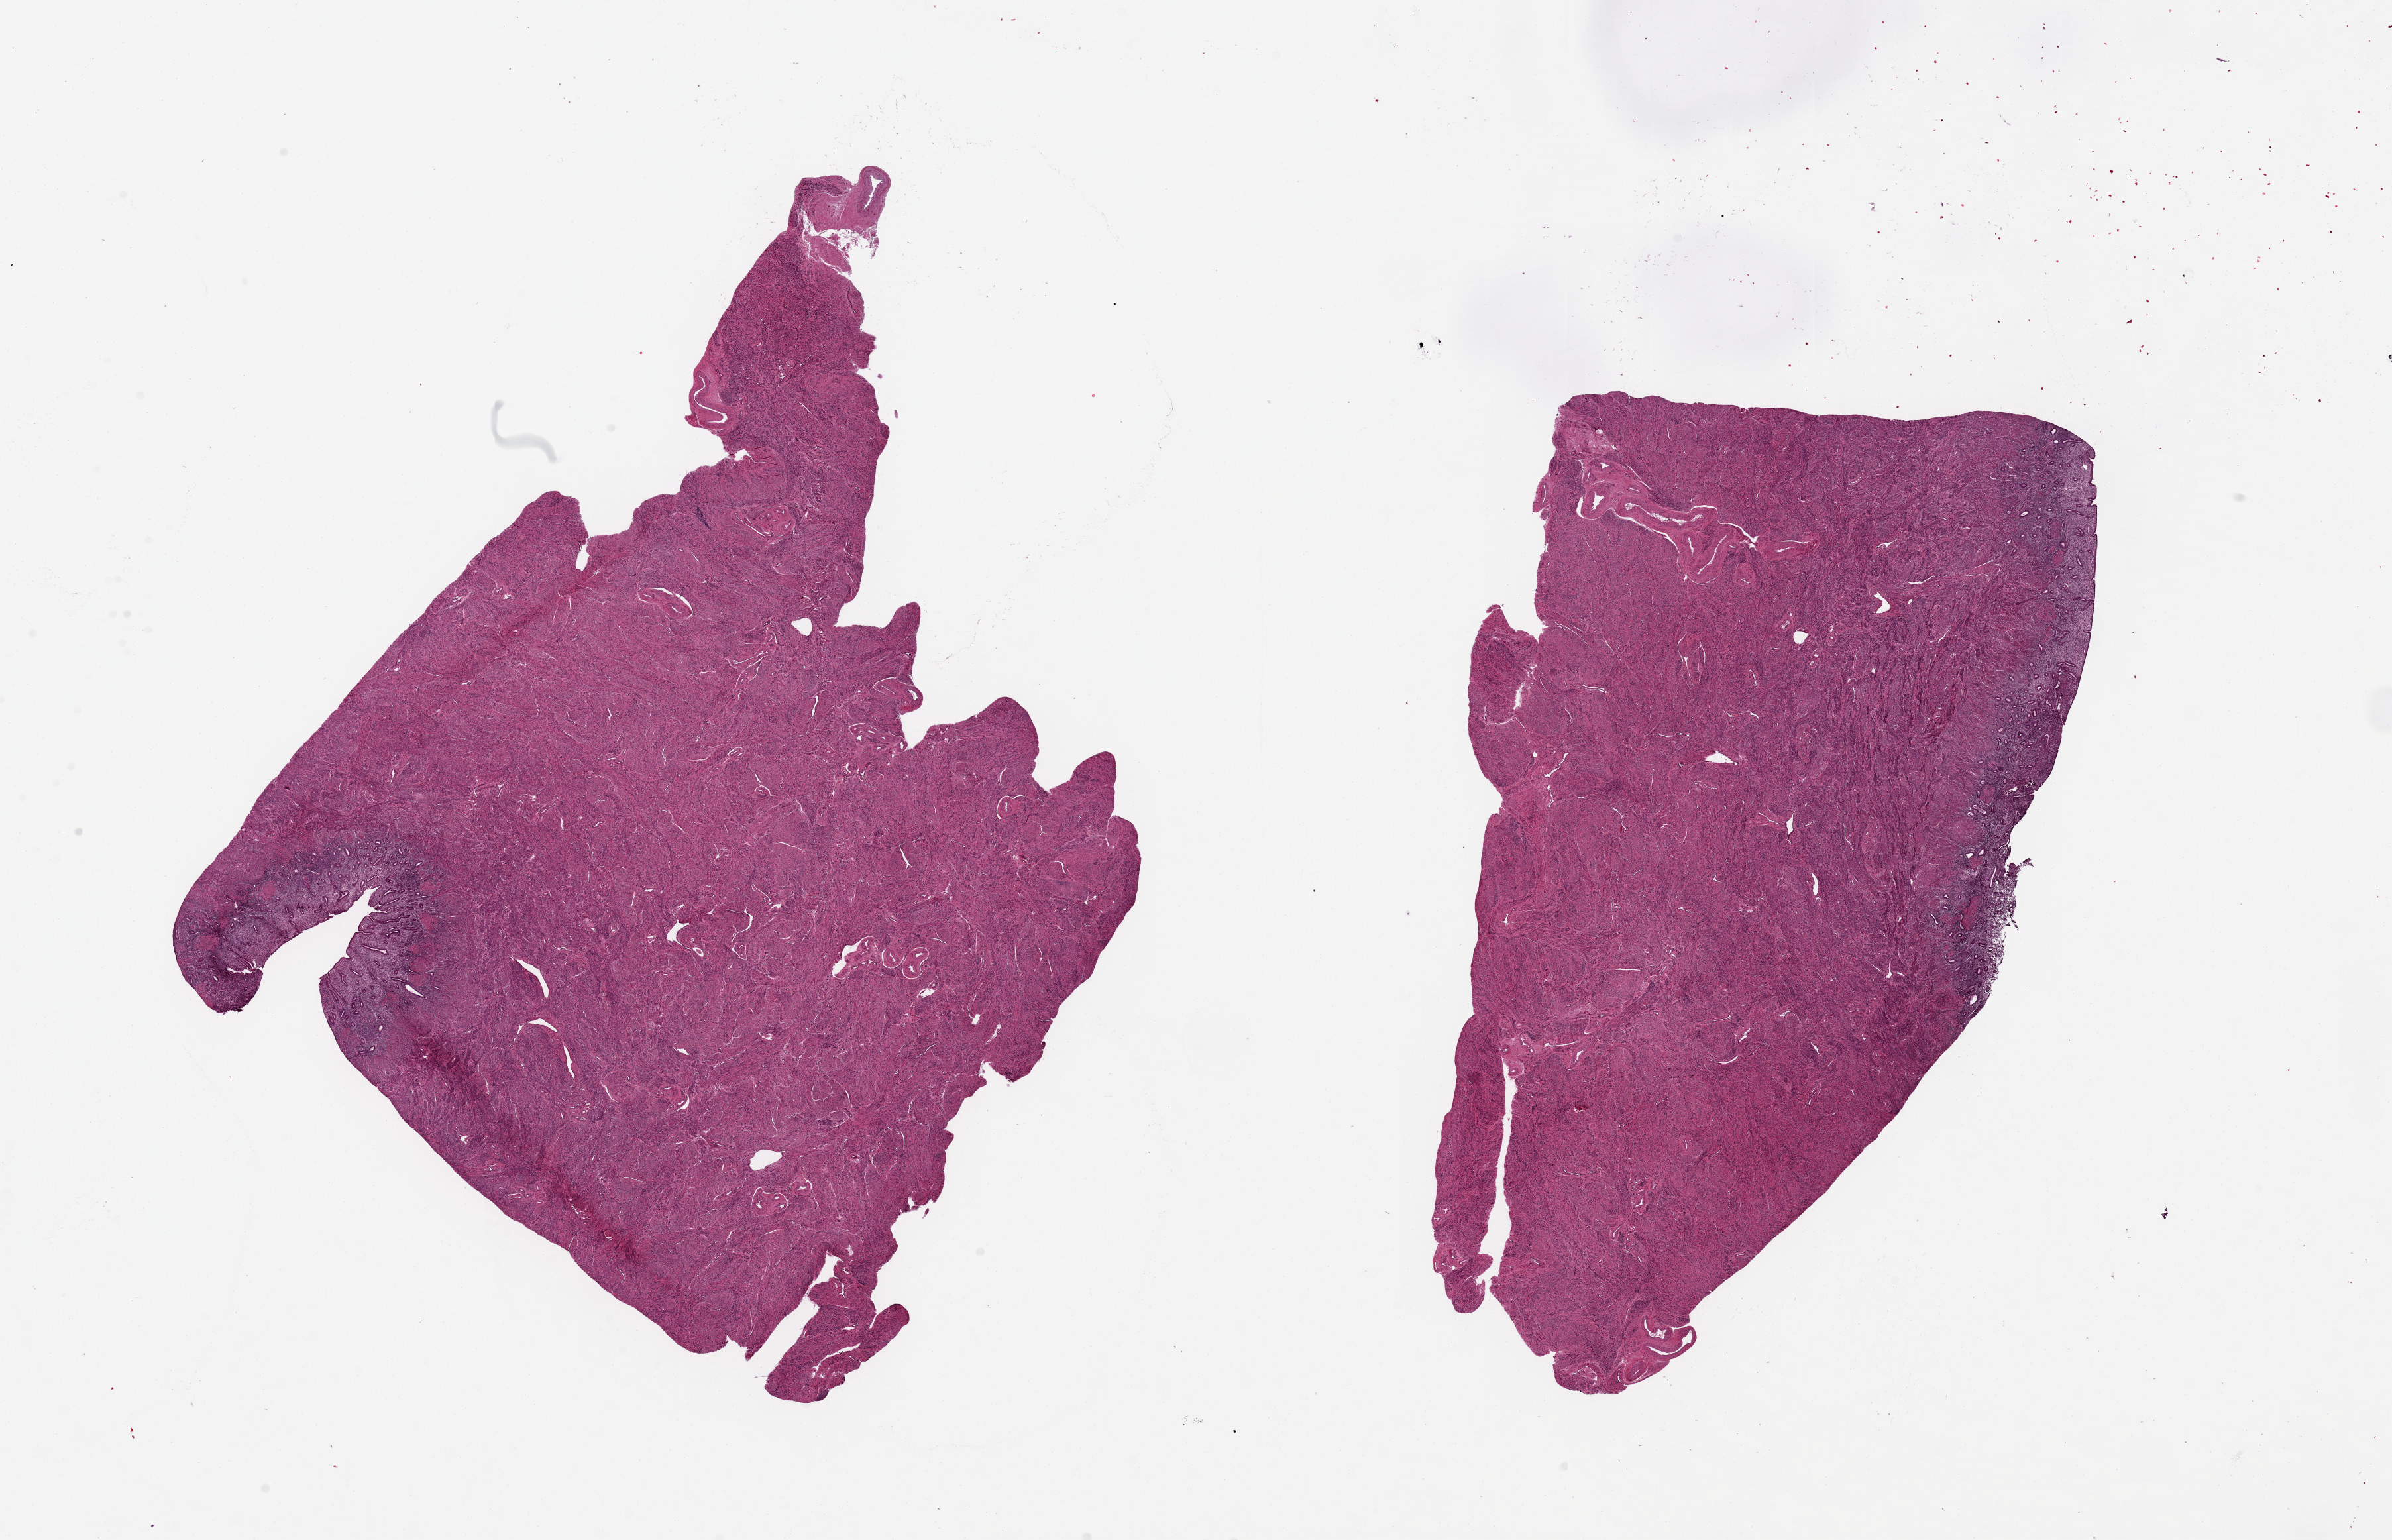
Hematoxylin and eosin (H&E) whole-slide image, brightfield — a low-resolution overview of the entire scanned area, about 28.5 x 18.4 mm (from a 20x scan); PAXgene-fixed, paraffin-embedded tissue; target tissue: uterus; tissue donor sample. Donor sex: female.
* review note (as recorded): 2 pieces, 13x10 & 12x7.5mm; 7-1mm proliferative endometrium